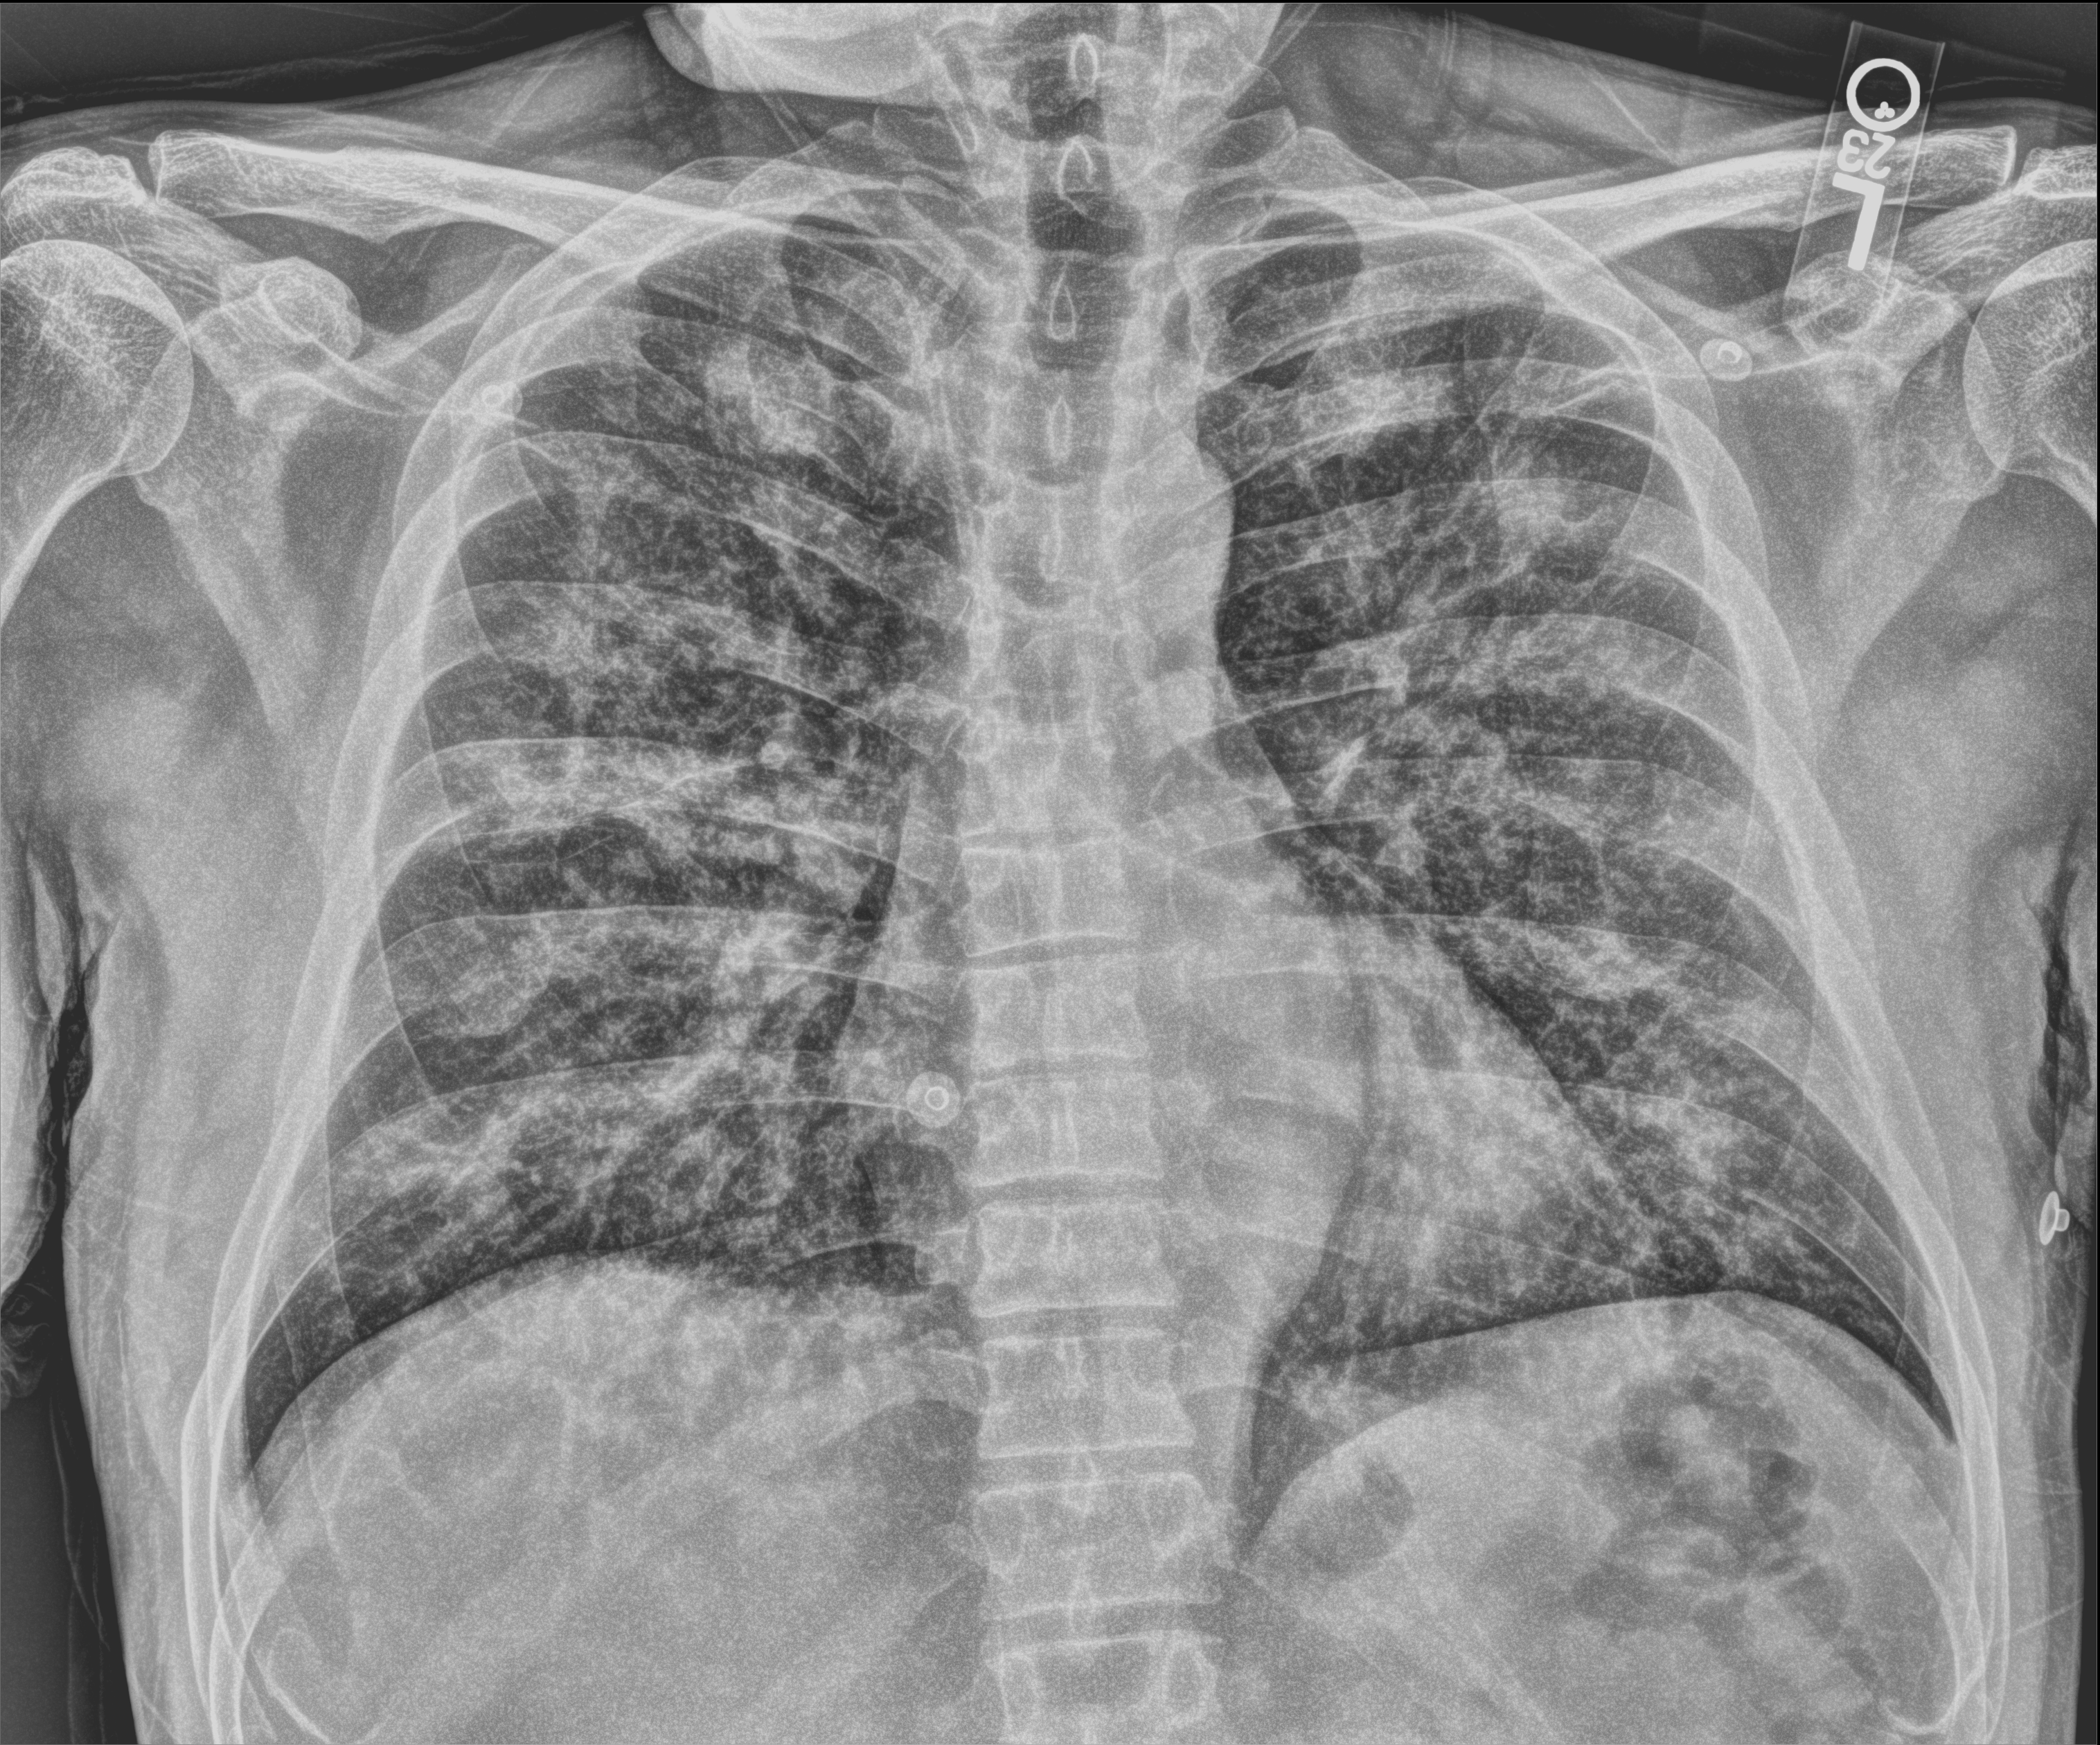
Chest X-ray (portable); anteroposterior (AP) projection. Male patient hospitalised with COVID-19, age 18–59 years.
From the hospital-stay record, not from the radiograph (when in the stay this image was taken is not recorded):
- mechanically ventilated during this hospital stay: no
- admitted to intensive care during this hospital stay: no